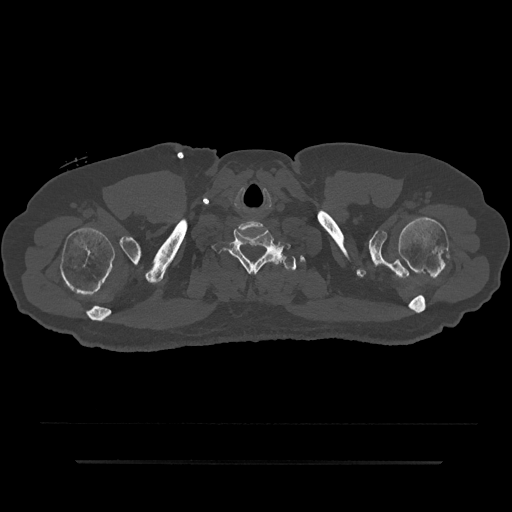
CT including the spine, one axial slice. Reconstruction kernel Br40s/3. Bone window (W 1800 / L 400 HU). 0.5 mm slice thickness. 512 × 512 image matrix, field of view 464 × 464 mm. Male patient, age 59 years. Case-level facts recorded for this patient, not image findings: primary cancer: bile ducts.
Structures marked on this image (semi-automatic segmentation, software-assisted and operator-edited):
- T1 vertebra: bounding box <272,252,305,271> (left, top, right, bottom; pixels)